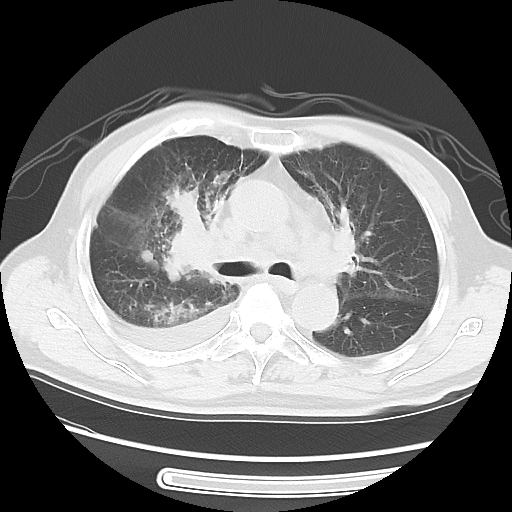
Chest CT, one axial slice. Slice 35 of 56 in the series (ordered by position). Lung window (W 1500 / L -600 HU). 5 mm slice thickness. 512 × 512 image matrix, field of view 360 × 360 mm. Male patient, age 77 years. Case-level facts recorded for this patient, not image findings: clinical TNM (as recorded): T3 N3 M1b; histopathological grade: G3.
Structures marked on this image (bounding box drawn by a radiologist):
- lung tumour (recorded histology: small cell carcinoma): bounding box (x1, y1, x2, y2) in pixels: (152, 176, 219, 286)